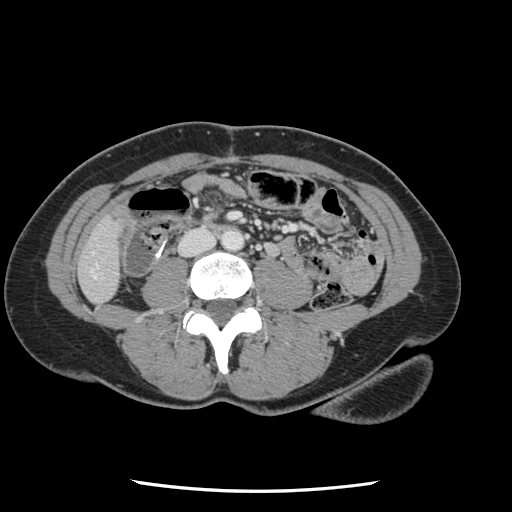
Contrast-enhanced abdominal CT, one axial slice; slice 8 of 134 in the series (ordered by position); intravenous contrast given; soft-tissue window (W 400 / L 40 HU); 2.5 mm slice thickness; 512 × 512 image matrix. Female patient, age 43 years. From the clinical record (not read from this slice): diagnosis: colorectal cancer liver metastases, imaged before liver resection.
Structures marked on this image (manually delineated by an expert):
- liver: box from (x=80, y=219) to (x=121, y=303) px
- planned liver remnant (the part of the liver to remain after resection): (x=80, y=218)–(x=120, y=303)